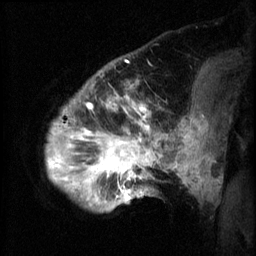
Breast MRI (dynamic contrast-enhanced), one sagittal slice; slice 13 of 60 in the series (ordered by position); 3 images stored at this slice position (order not interpretable as contrast timing); 1.5 T; TE 4.2 ms, TR 8.2 ms; 2.3 mm slice thickness; 256 × 256 image matrix, field of view 200 × 200 mm. Female patient, age 50 years.
Structures marked on this image (semi-automatic segmentation, software-assisted and operator-edited):
- analysis volume of interest (the breast-tissue region the enhancement analysis was run in; not a lesion): bounding box <50,64,169,213> (left, top, right, bottom; pixels)
- tumour enhancement mask (voxels above the 70 % enhancement threshold inside the analysis volume of interest): <50,96,163,207>